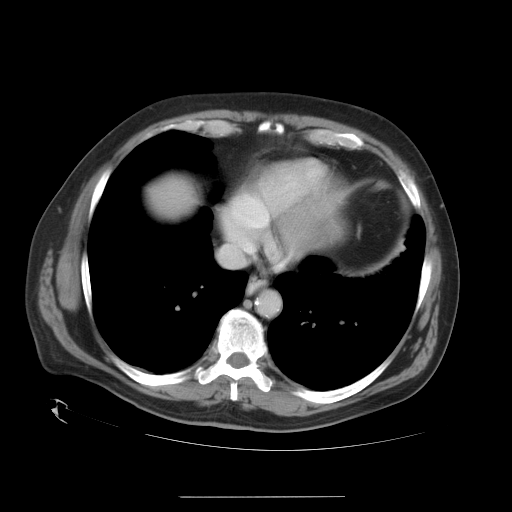
Contrast-enhanced abdominal CT, one axial slice; position 32 of 35 along the scan axis; reconstruction kernel STANDARD; 120 kVp; intravenous contrast given; soft-tissue window (W 400 / L 40 HU); 512 × 512 image matrix, field of view 450 × 450 mm. Male patient, age 67 years. Case-level facts recorded for this patient, not image findings: diagnosis: colorectal cancer liver metastases, imaged before liver resection; multiple liver metastases: no; largest metastasis: 2.3 cm; disease in both lobes: no.
Structures marked on this image (expert manual segmentation):
- liver: bounding box (x1, y1, x2, y2) in pixels: (154, 179, 187, 217)
- planned liver remnant (the part of the liver to remain after resection): (153, 180, 187, 217)